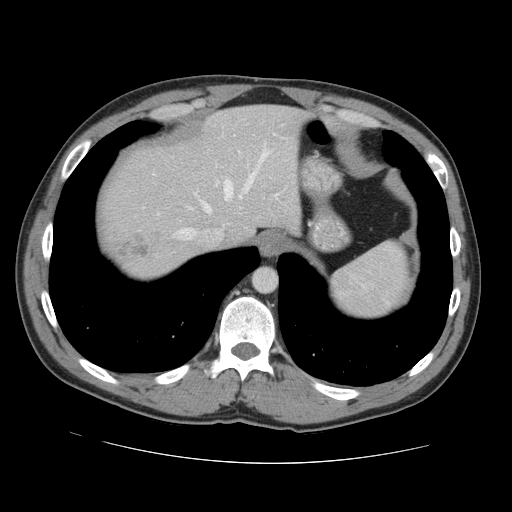
Contrast-enhanced abdominal CT, one axial slice. Position 117 of 131 along the scan axis. 120 kVp. Intravenous contrast given. Soft-tissue window (W 400 / L 40 HU). 2.5 mm slice thickness. 512 × 512 image matrix, field of view 380 × 380 mm. Male patient, age 40 years. From the clinical record (not read from this slice): diagnosis: colorectal cancer liver metastases, imaged before liver resection; multiple liver metastases: yes; largest metastasis: 2.9 cm.
Outlined on this slice (expert manual segmentation):
- hepatic veins: box from (x=178, y=152) to (x=268, y=239) px
- liver: (x=99, y=106)–(x=304, y=277)
- planned liver remnant (the part of the liver to remain after resection): (x=120, y=106)–(x=304, y=243)
- liver metastasis: (x=118, y=234)–(x=151, y=258)